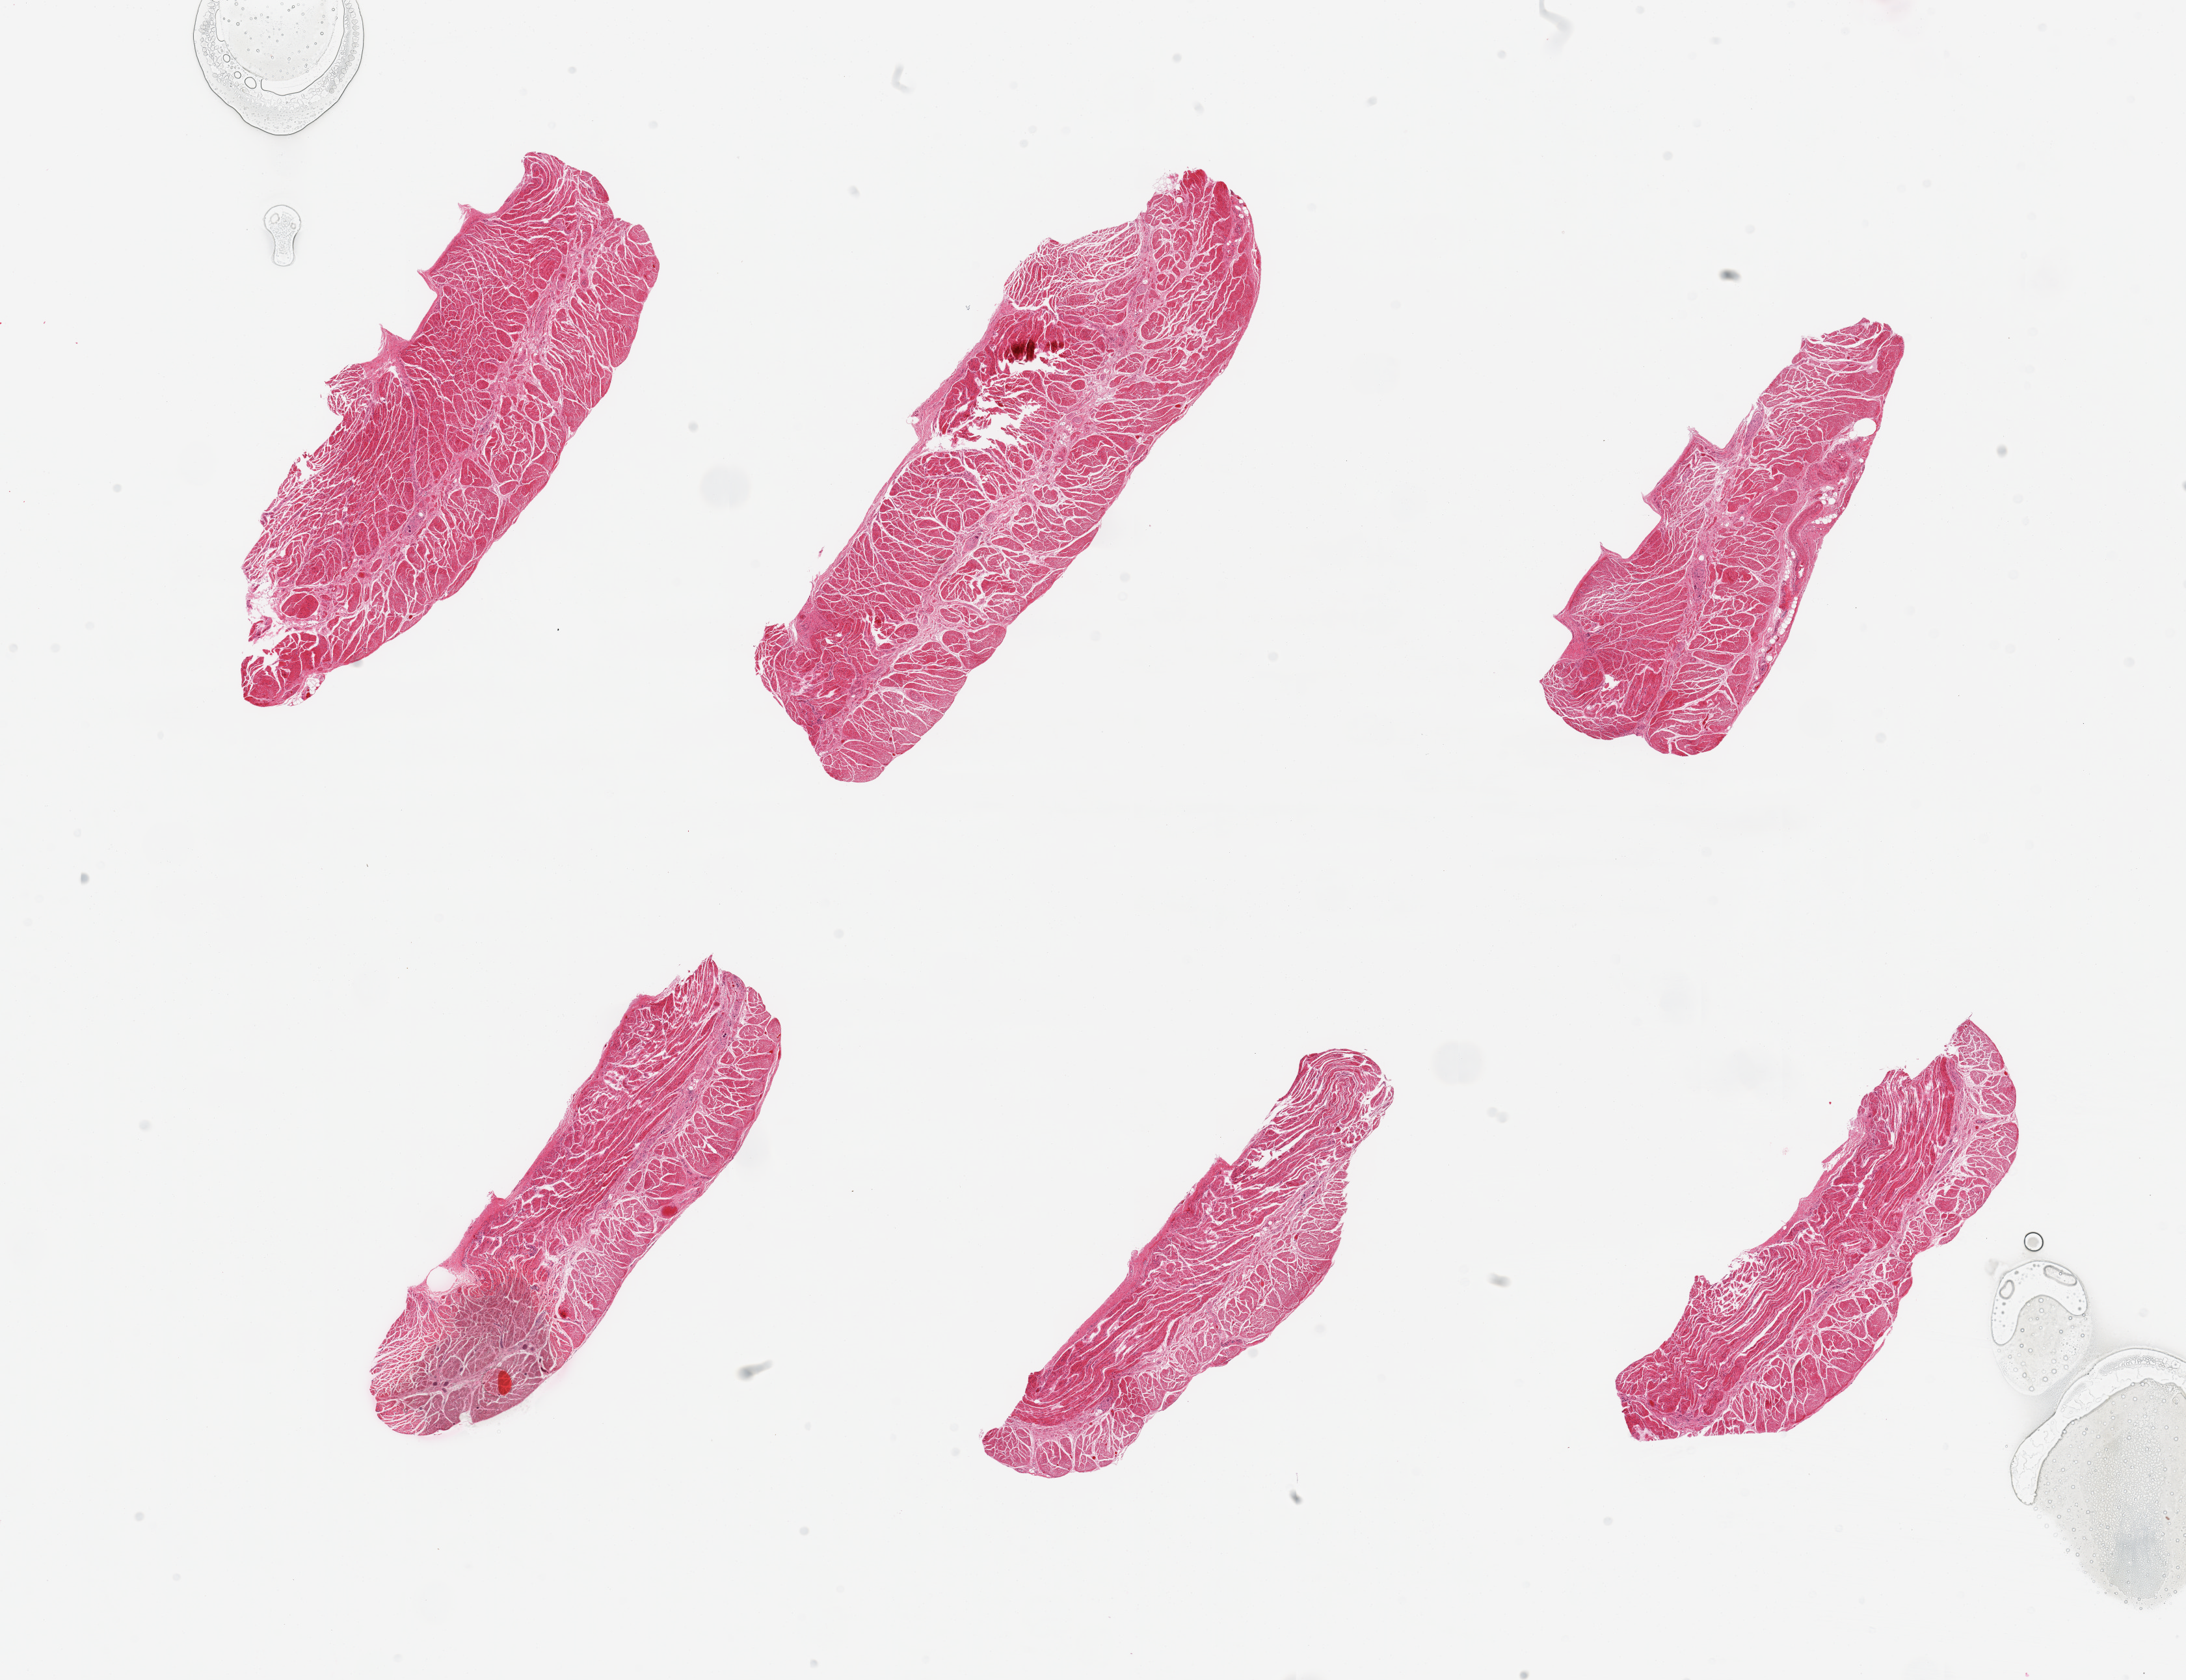
Haematoxylin and eosin whole-slide image, shown as a low-resolution overview of the whole scanned area (about 26.6 x 20.4 mm). PAXgene-fixed, paraffin-embedded tissue. Section of esophageal muscle (target tissue). Tissue donor sample.
• pathologist's review note for this sample: 6 pieces; well trimmed